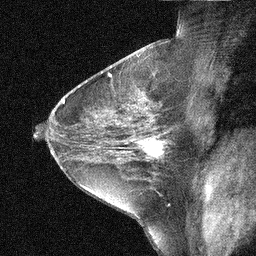
Breast MRI (dynamic contrast-enhanced), one sagittal slice; slice 26 of 44 in the series (ordered by position); dynamic contrast-enhanced study with each time point stored as its own series, time point 2 of 3 at this slice position (early post-contrast, ordered by acquisition time); 1.5 T; TE 5 ms, TR 10.3 ms; 256 × 256 image matrix, field of view 180 × 180 mm. Patient: female, 31 years. Case-level facts recorded for this patient, not image findings: setting: breast cancer imaged before/during neoadjuvant chemotherapy; receptor status: HER2-positive.
Structures marked on this image (semi-automatic segmentation, software-assisted and operator-edited):
- analysis volume of interest (the breast-tissue region the enhancement analysis was run in; not a lesion): box from (x=136, y=131) to (x=181, y=168) px
- tumour enhancement mask (voxels above the 90 % enhancement threshold inside the analysis volume of interest): (x=138, y=137)–(x=167, y=160)